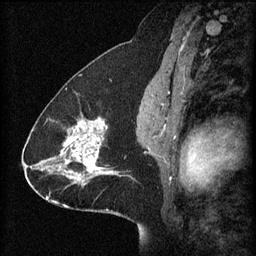
Breast MRI (dynamic contrast-enhanced), one sagittal slice. Position 36 of 60 along the scan axis. 3 images stored at this slice position (order not interpretable as contrast timing). 1.5 T. TE 4.2 ms, TR 8.2 ms. 2 mm slice thickness. 256 × 256 image matrix. Patient: female, 41 years.
Annotated regions visible in this slice (semi-automatically segmented with operator editing):
- analysis volume of interest (the breast-tissue region the enhancement analysis was run in; not a lesion): bounding box <58,112,128,181> (left, top, right, bottom; pixels)
- tumour enhancement mask (voxels above the 70 % enhancement threshold inside the analysis volume of interest): <62,118,114,181>